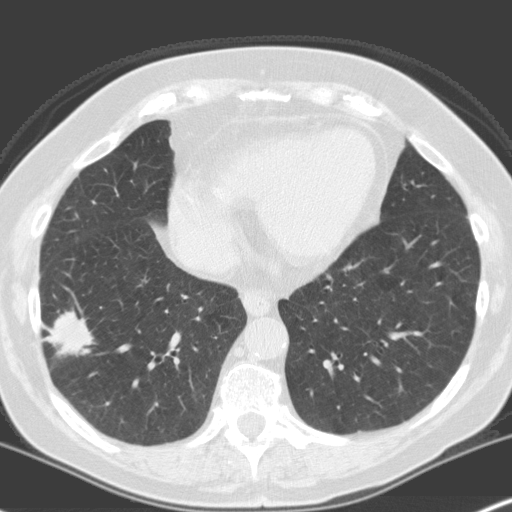
Axial slice from a low-dose chest CT screening exam; first (baseline) screen; lung window (W 1500 / L -600 HU); slice 97 of 160 in the series. Female, age 70 years at enrolment. Current smoker at enrolment.
Expert-annotated lung lesion, bounding box <31,299,100,368> (left, top, right, bottom; pixels). The screening reader recorded 4 non-calcified nodules or masses ≥4 mm on this exam (right lower lobe, right upper lobe, left upper lobe, left upper lobe); which of them this box marks is not recorded. Later outcome: lung cancer diagnosed 28 days after this screen — adenocarcinoma, NOS, right lower lobe, moderately differentiated (G2), stage IV (AJCC 6th edition), 28 mm at pathology.